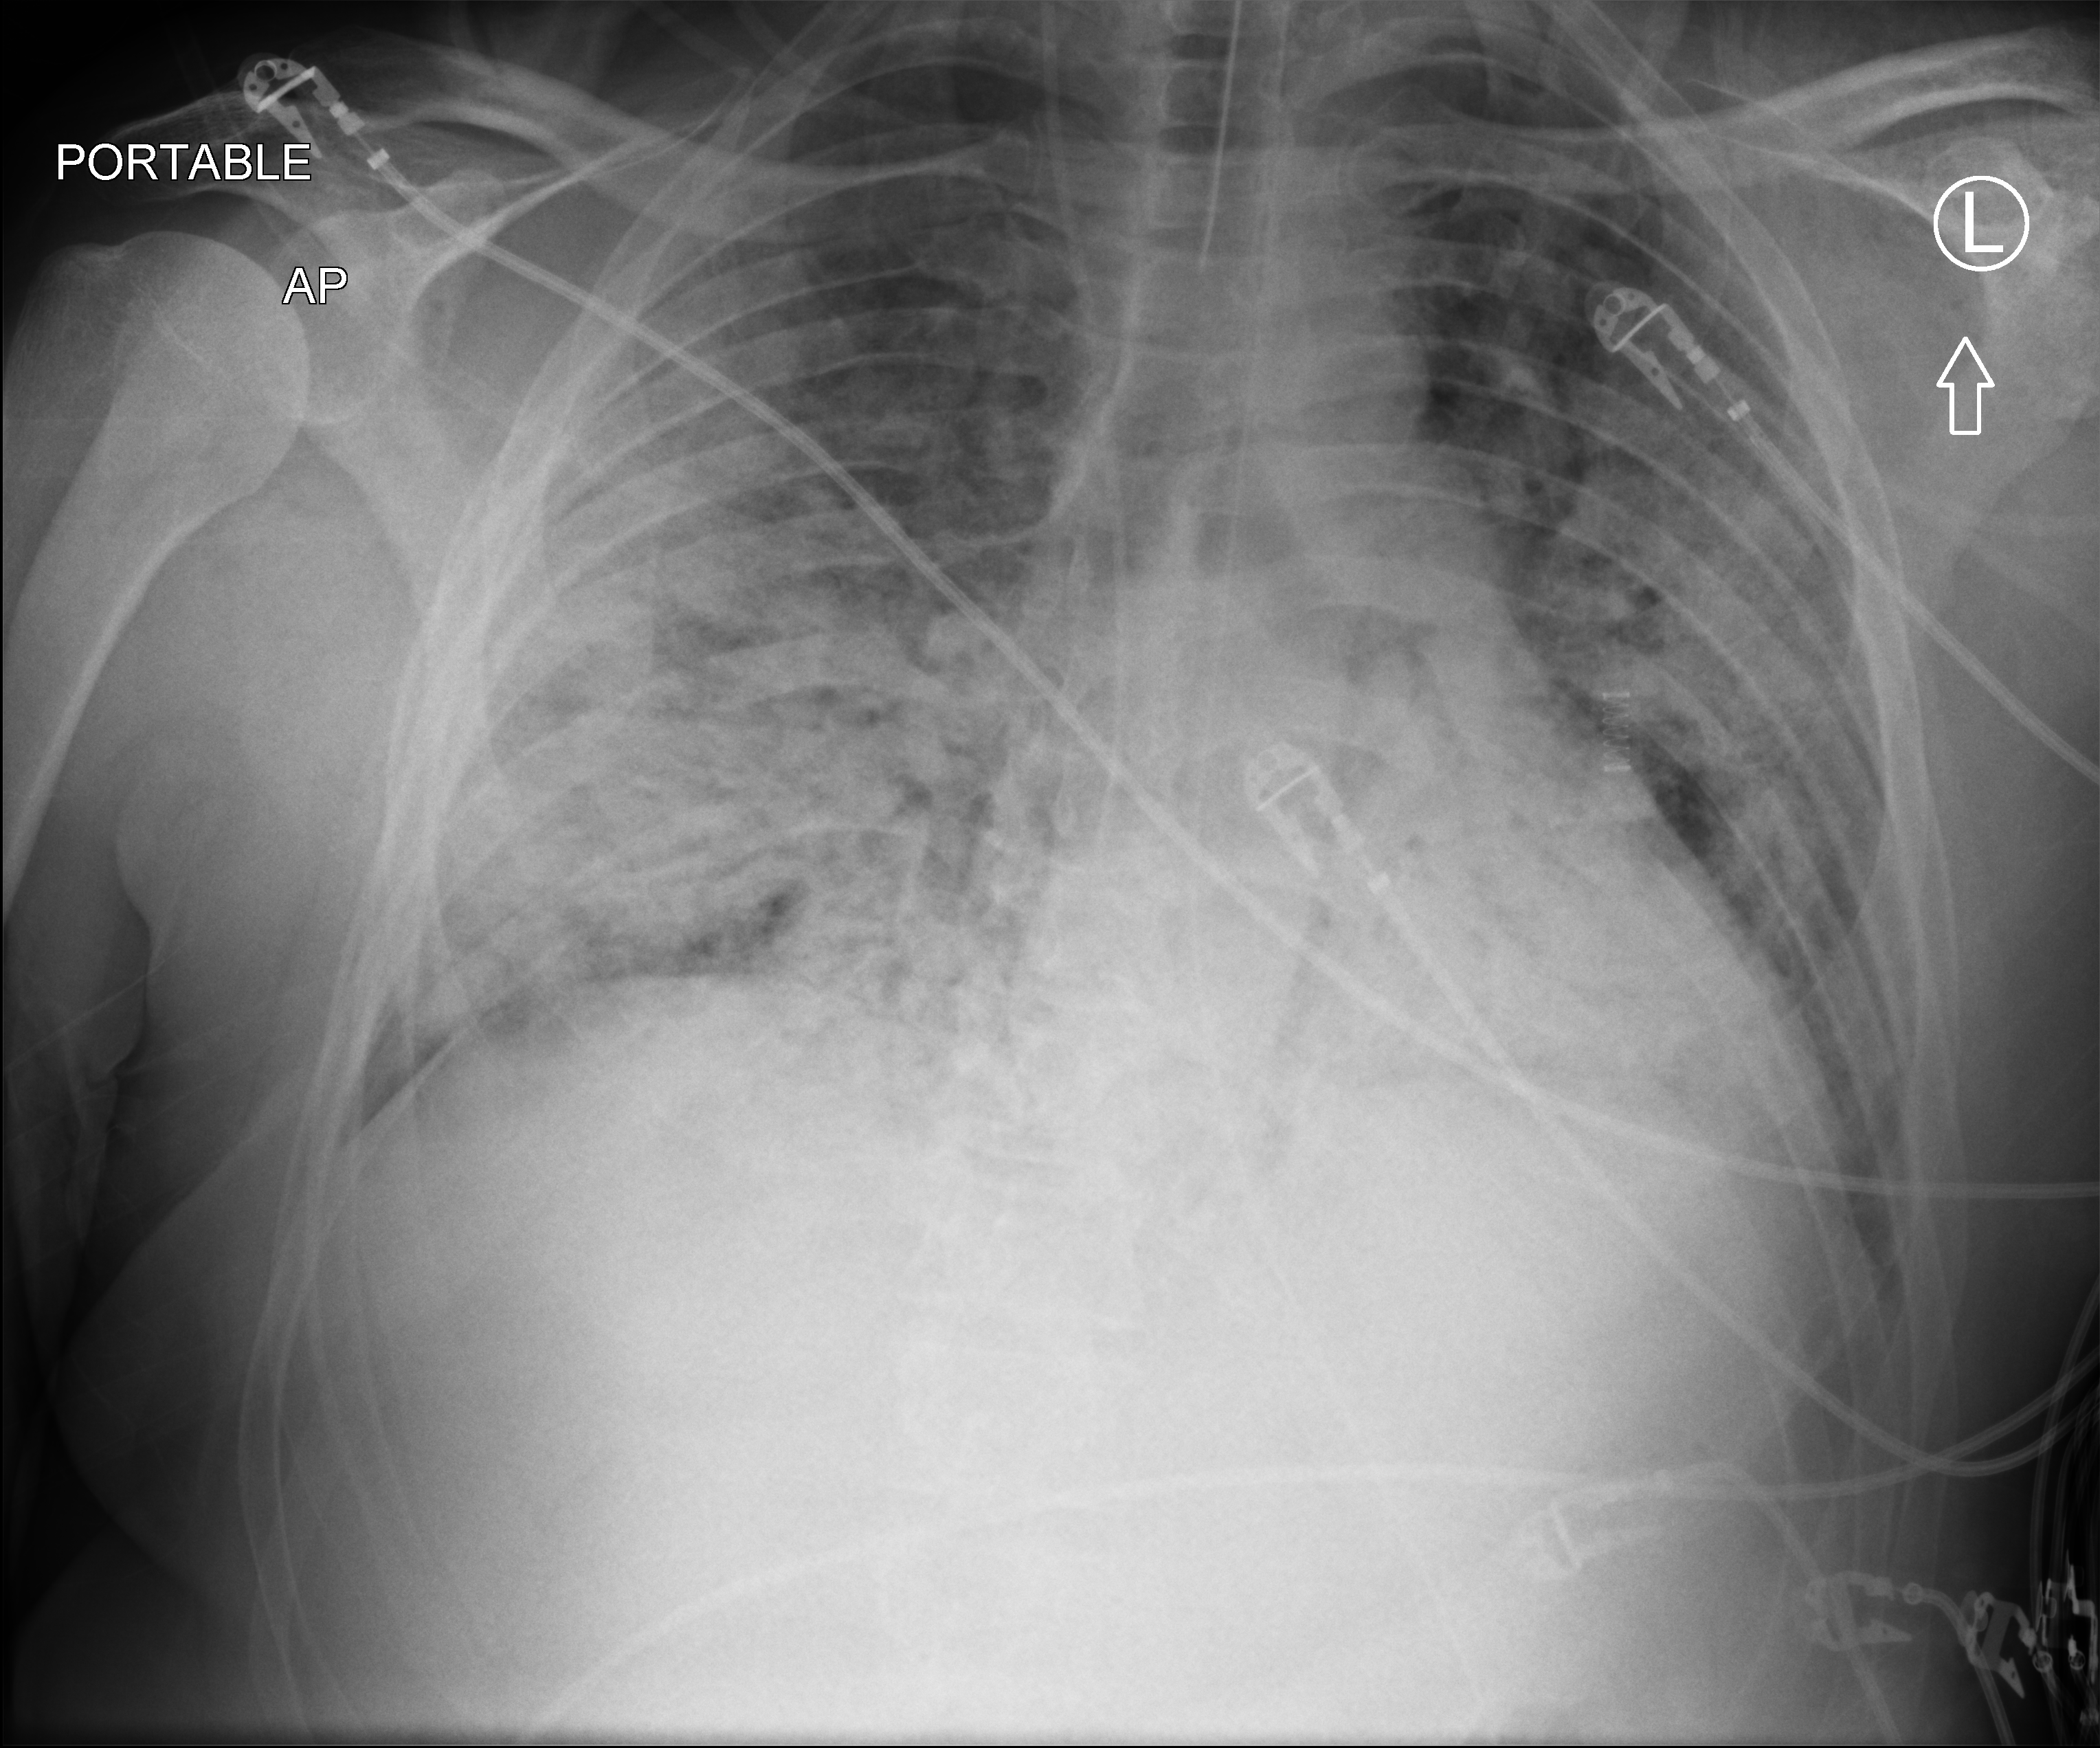
Chest X-ray (portable), anteroposterior (AP) projection. Male patient hospitalised with COVID-19, age 18–59 years.
From the hospital-stay record, not from the radiograph (when in the stay this image was taken is not recorded): chronic kidney disease (admission record): no.